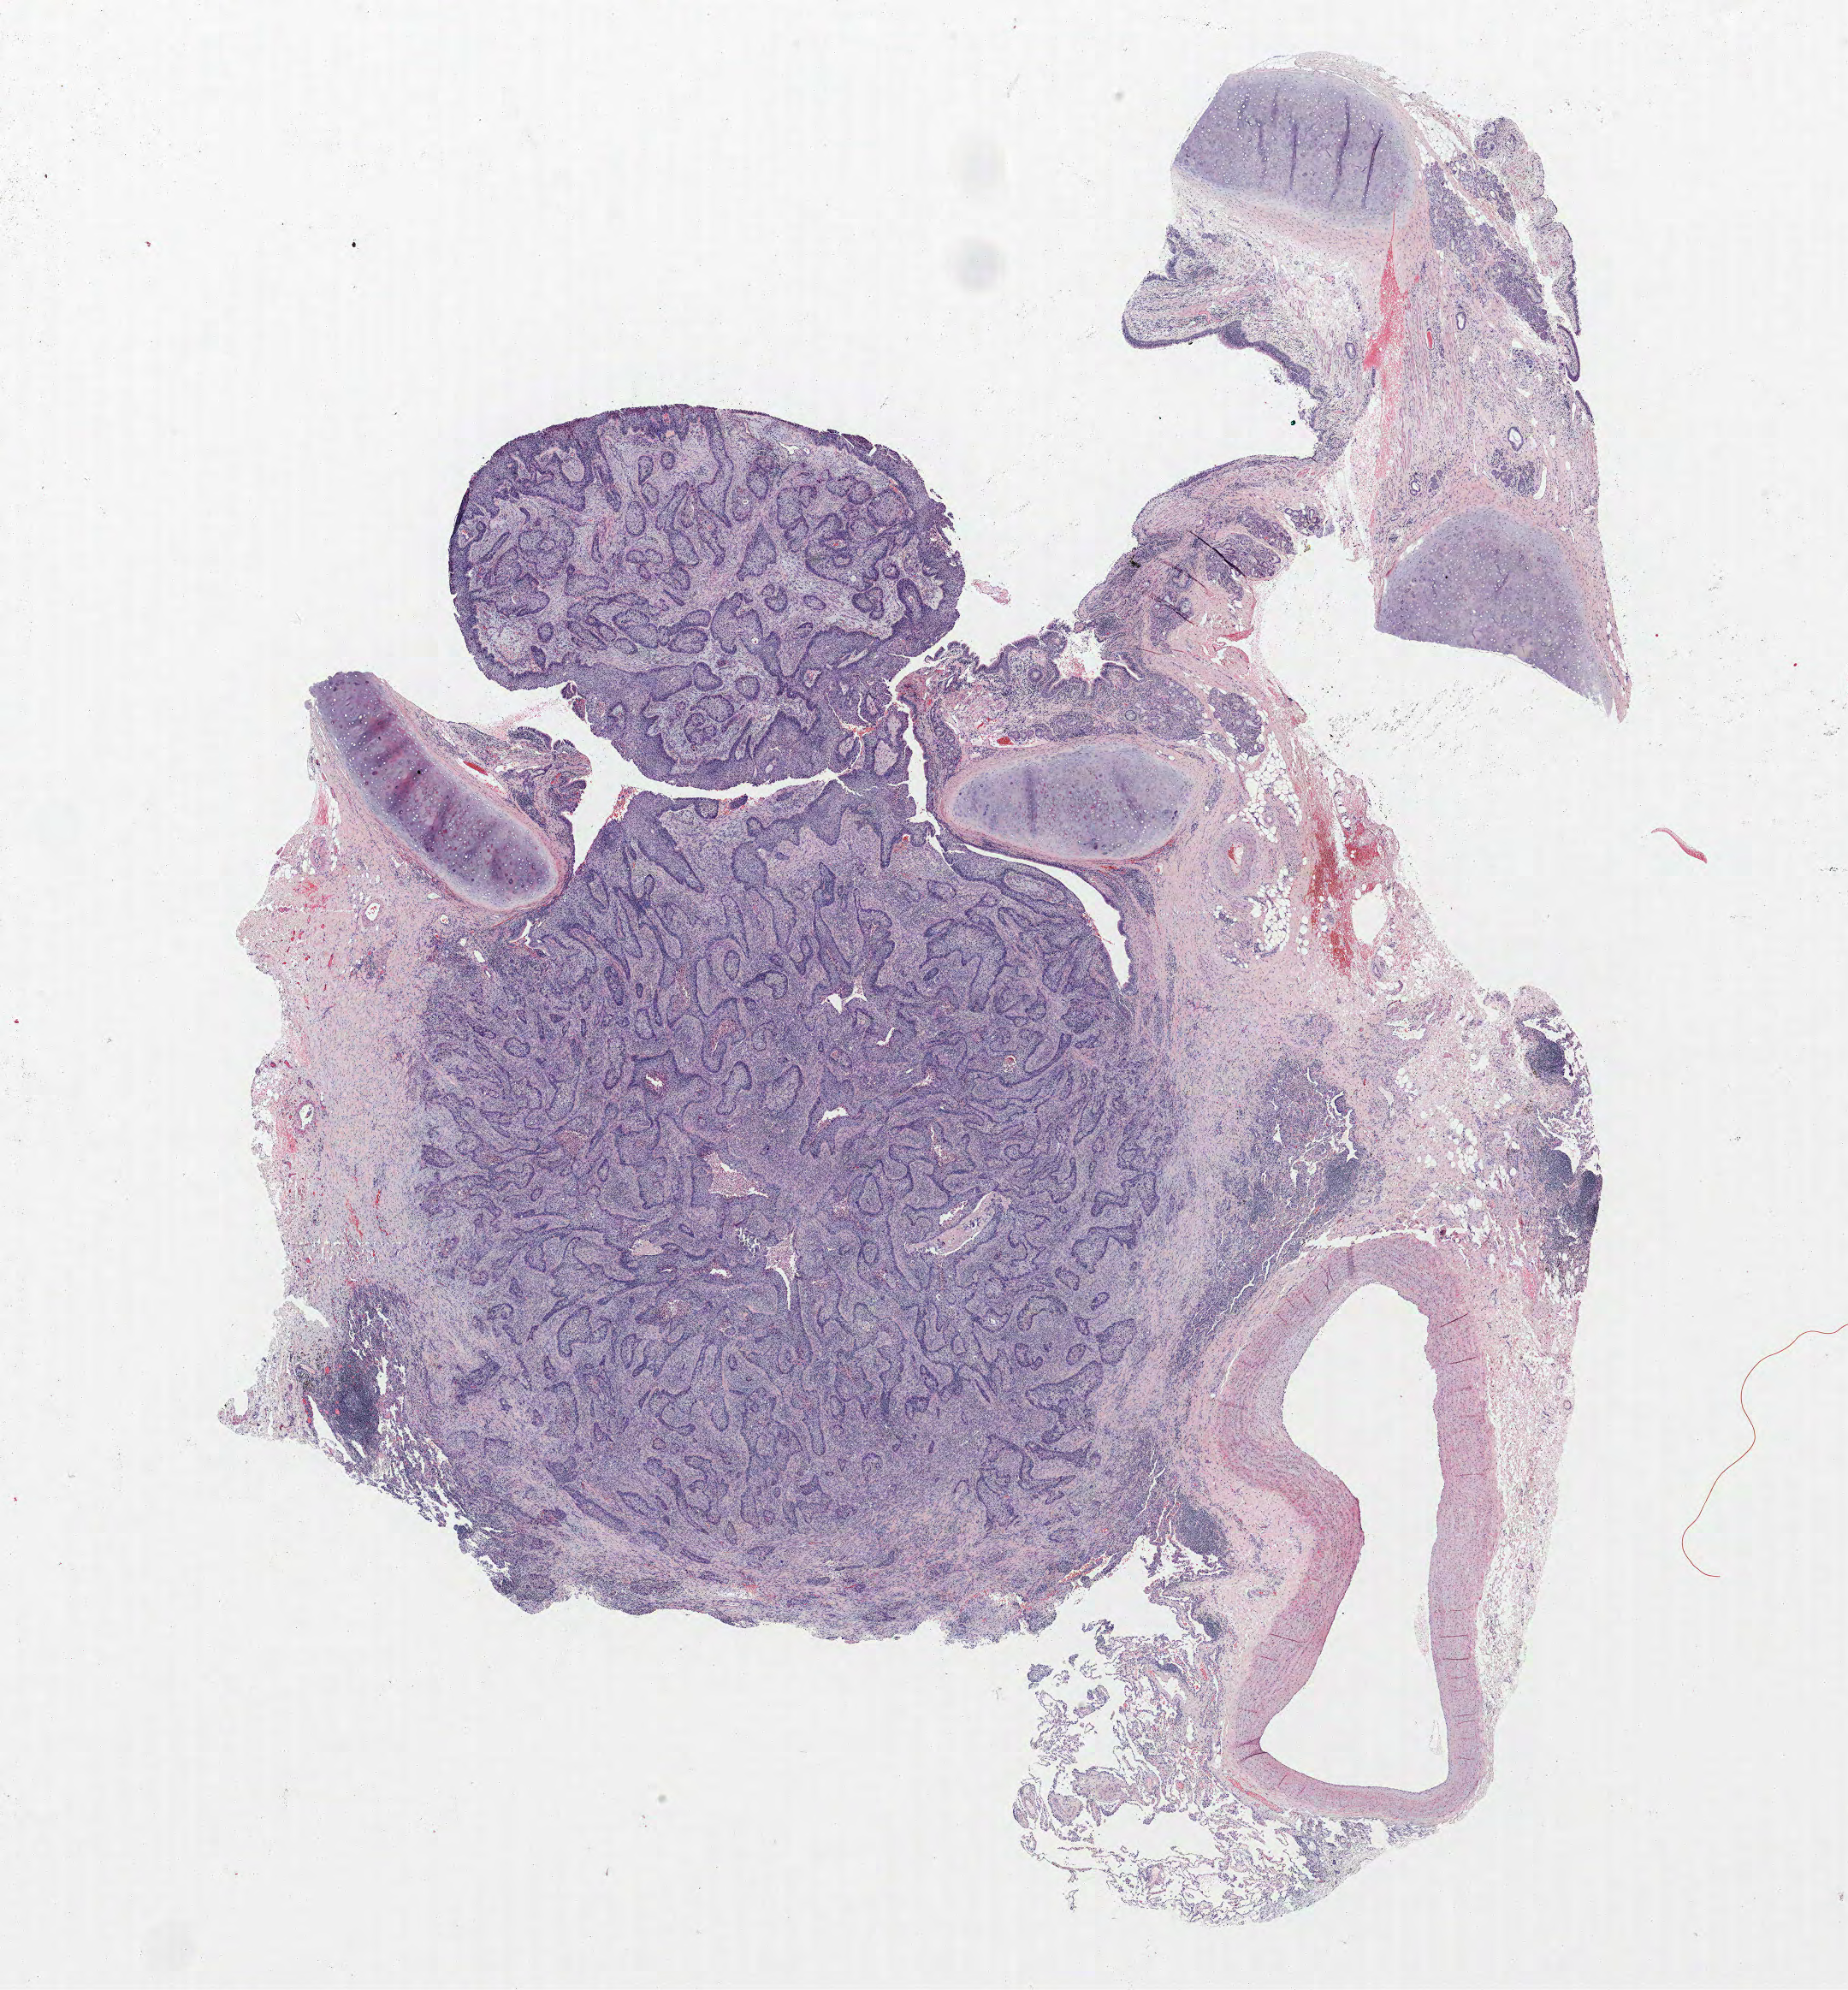
Whole-slide histology image, H&E, a low-resolution overview of the entire scanned area, about 17.3 x 18.6 mm, formalin-fixed paraffin-embedded (FFPE) section, lung tissue. Male patient, aged 63 at enrolment. Former smoker at enrolment. Grade: moderately differentiated (G2).
ICD-O-3 topography: upper lobe of lung (C34.1). Participant's lung-cancer diagnosis: Squamous cell carcinoma, NOS. Primary tumour location (clinical record): left upper lobe. Stage (AJCC 6th edition): IA. Tumour size (pathology): 23 mm.